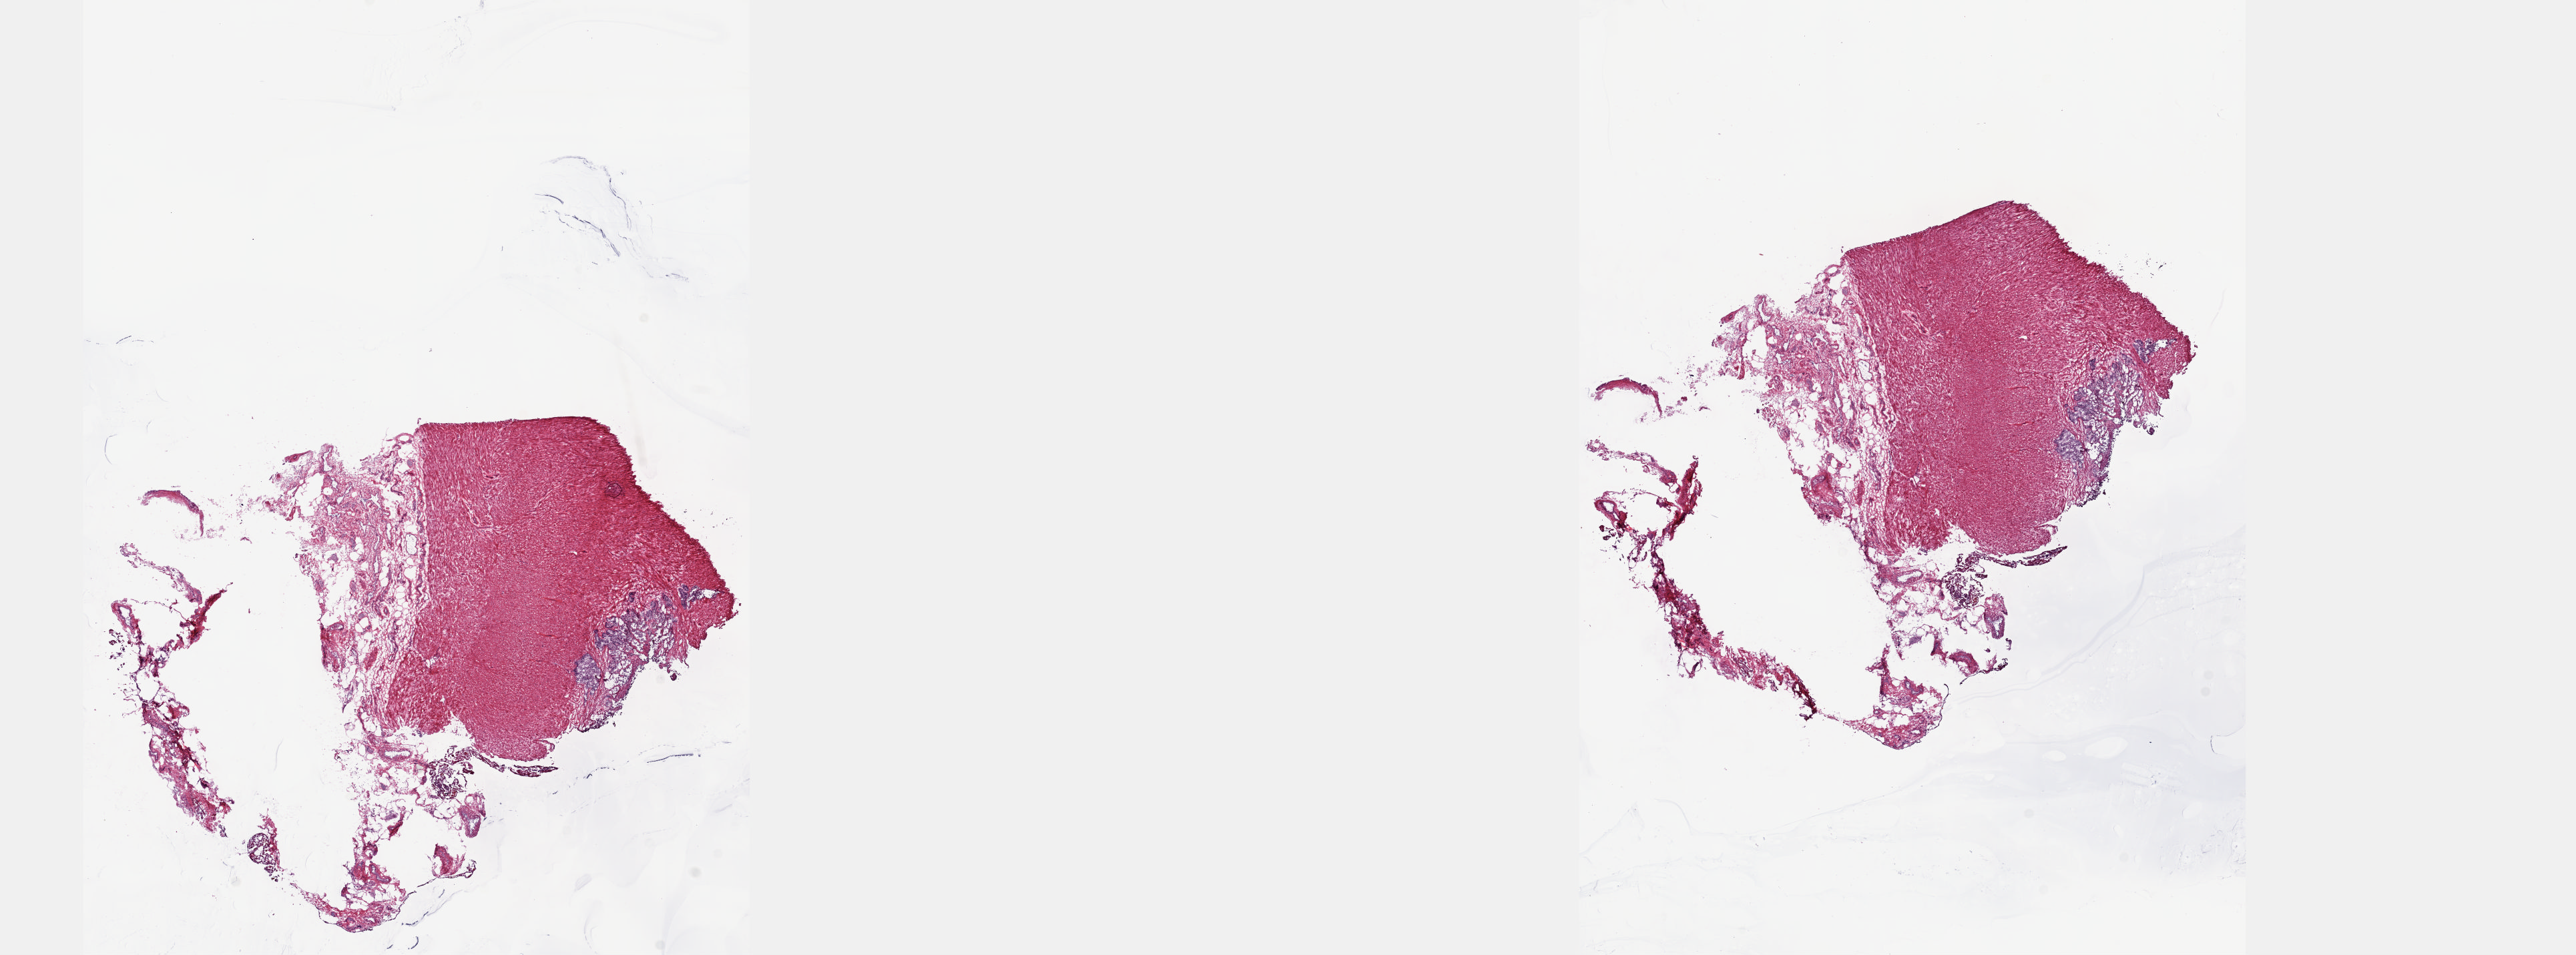
H&E whole-slide image — whole scanned area (about 31.1 x 11.5 mm) shown as a low-resolution overview; frozen section; sample: solid tissue normal (non-tumour tissue), prostate. Male, age 61 years at initial diagnosis. Slide review estimates, as recorded: tumour cells 0%, tumour nuclei 0%, normal cells 10%, stromal cells 90%, necrosis 0%. Infiltration values recorded for this section: lymphocyte infiltration 0%, monocyte infiltration 0%, neutrophil infiltration 0%.
This section: solid tissue normal sample (biorepository sample class). Patient diagnosis: Infiltrating duct carcinoma, NOS (prostate gland).